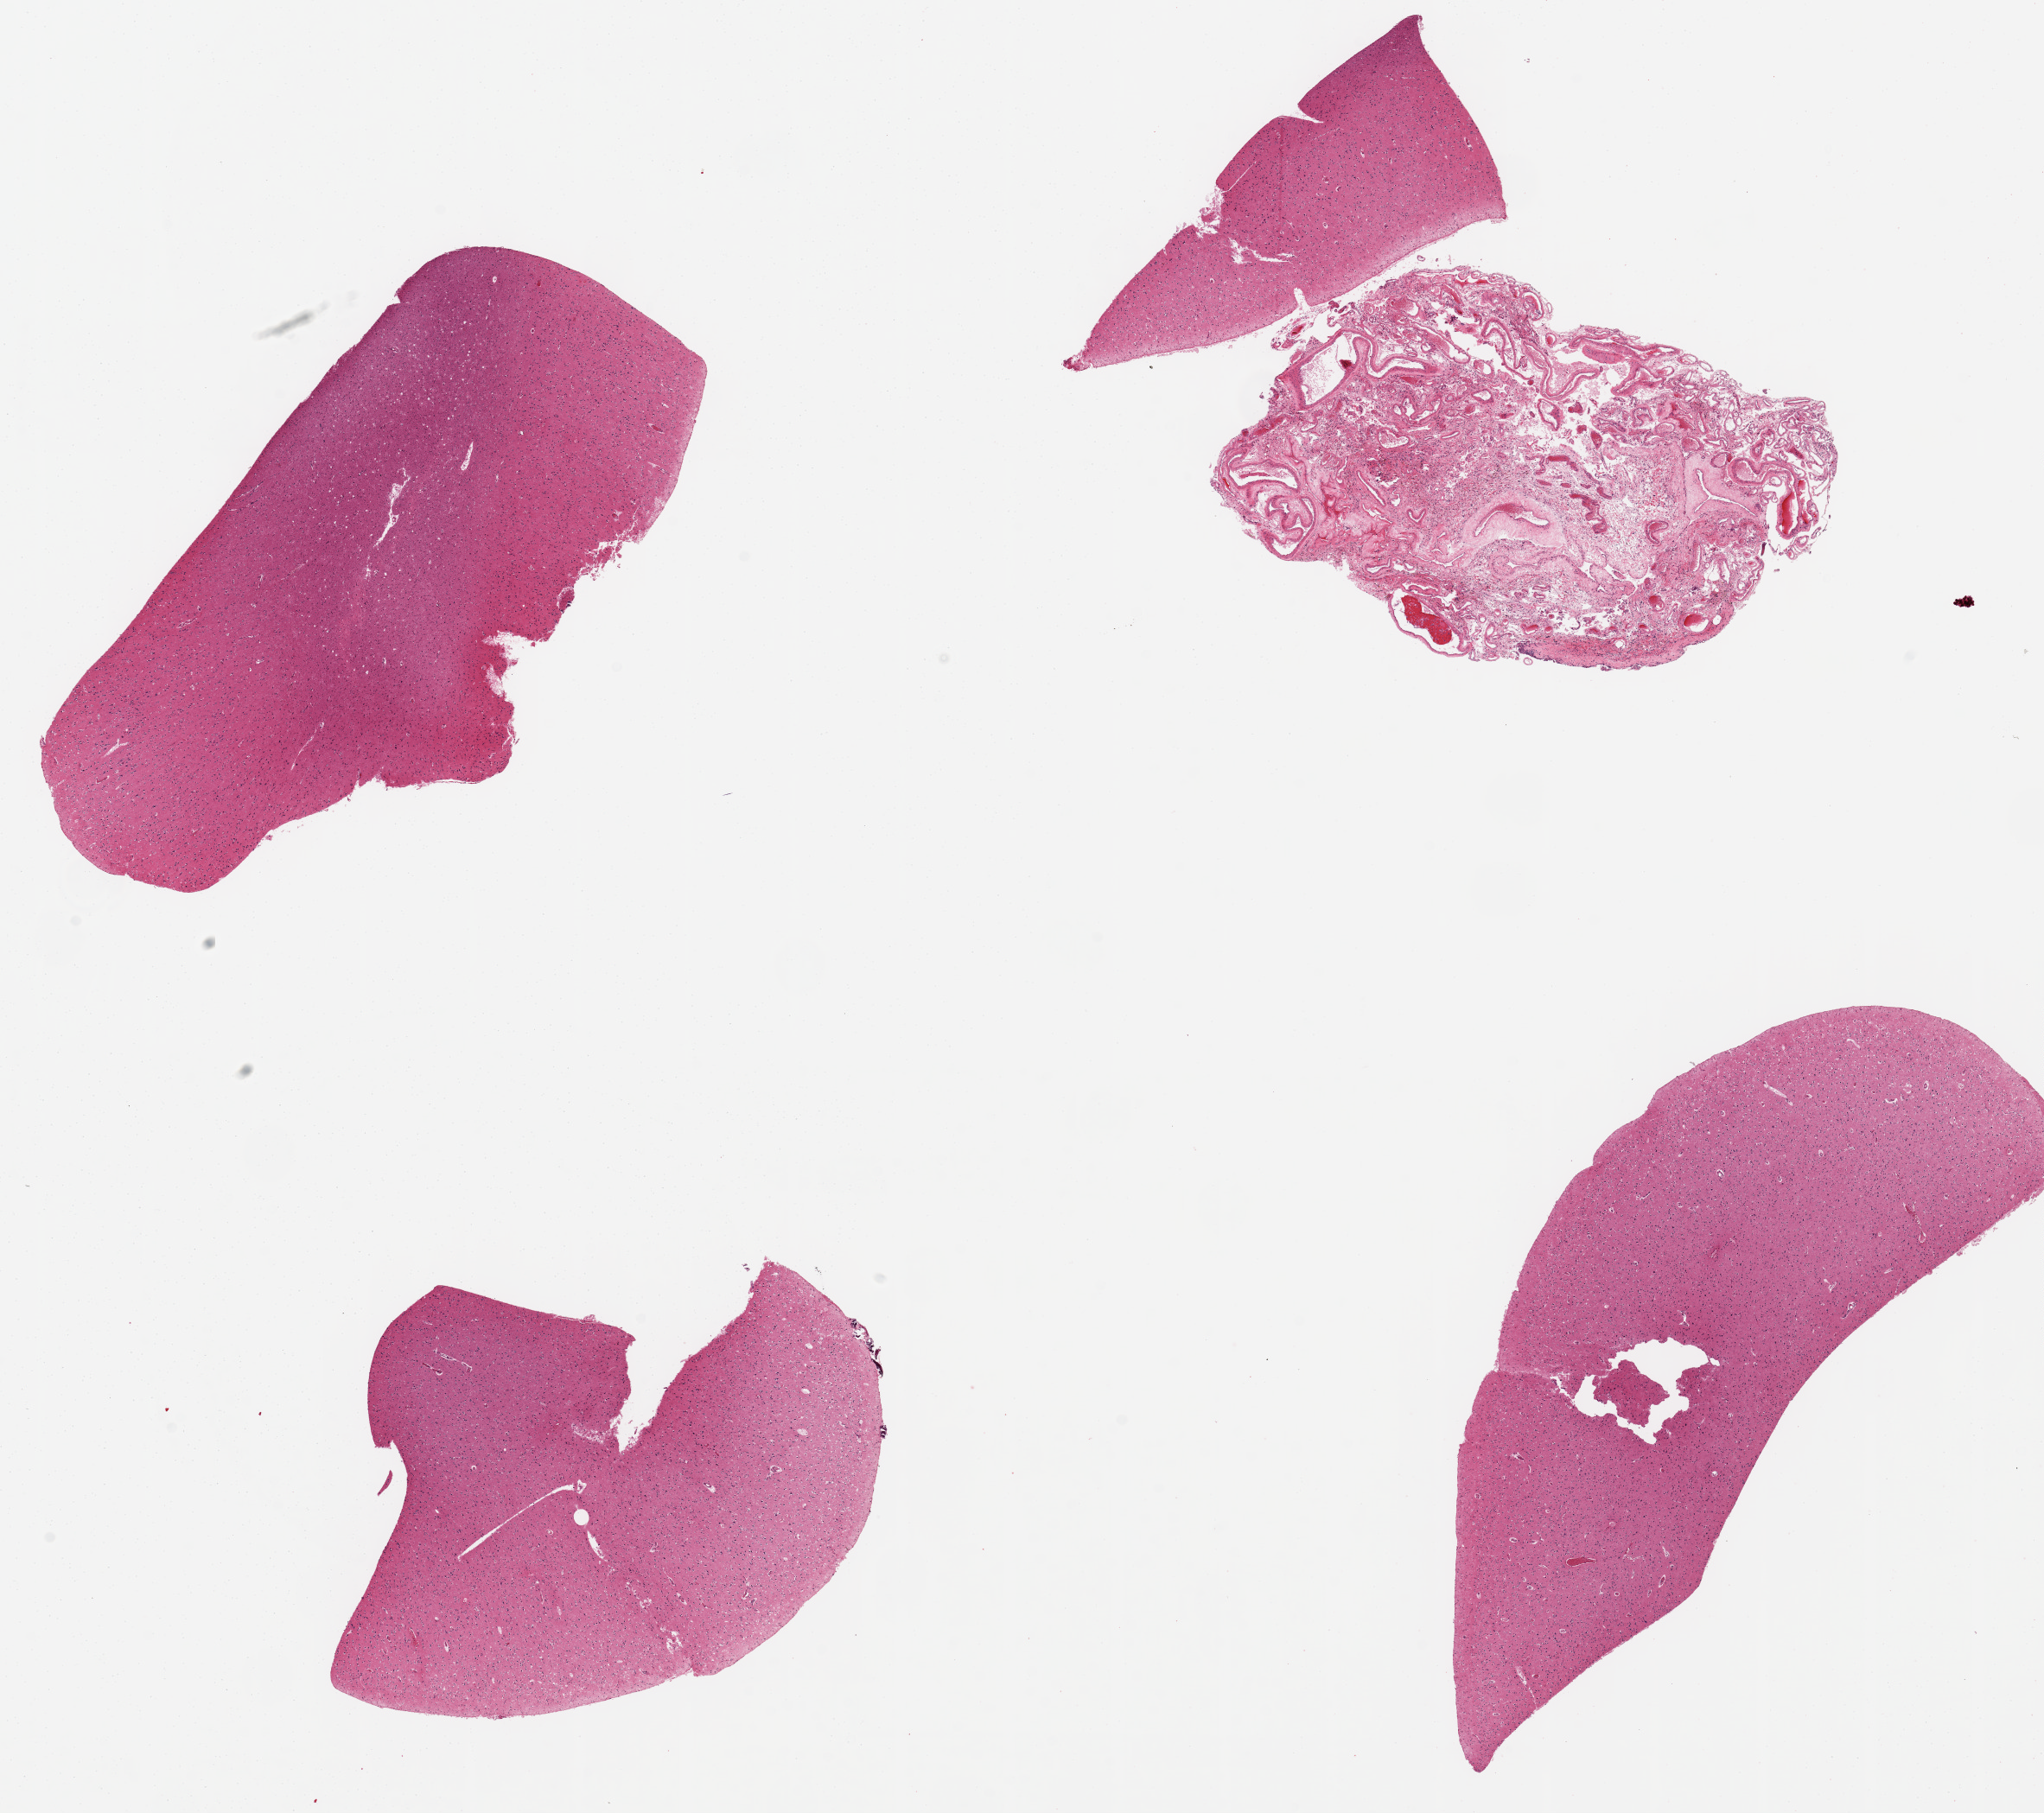
Hematoxylin and eosin (H&E) whole-slide image, a low-resolution overview of the entire scanned area, about 18.7 x 16.6 mm (acquisition: 20x scan); PAXgene-fixed, paraffin-embedded tissue; sampled site (target tissue): cerebral cortex; donor tissue sample.
Reviewer comment on this tissue sample: 3 ~7x3 mm aliquots; 1 ~4x1.5mm aliquot; 1 ~3.5x3.5mm fragment of dura.